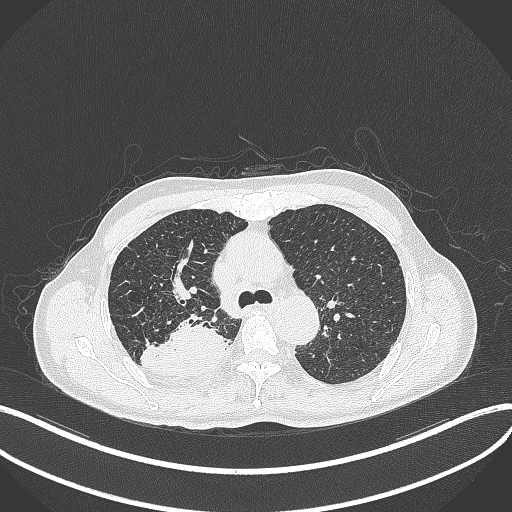
Chest CT, one axial slice; slice 312 of 428 in the series (ordered by position); 120 kVp; lung window (W 1500 / L -600 HU); 1 mm slice thickness; 512 × 512 image matrix, field of view 400 × 400 mm. Male patient, age 79 years. Case-level facts recorded for this patient, not image findings: clinical TNM (as recorded): T3 N0 M0.
Structures marked on this image (bounding box drawn by a radiologist):
- lung tumour (recorded histology: adenocarcinoma): bounding box (x1, y1, x2, y2) in pixels: (138, 309, 229, 380)